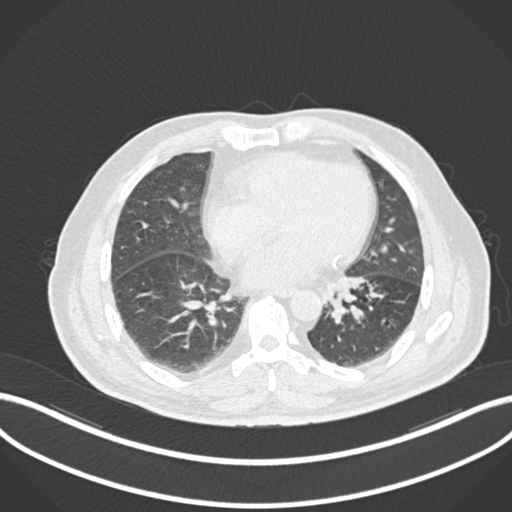
Chest CT, one axial slice. Position 41 of 161 along the scan axis. Reconstruction kernel B30f. Lung window (W 1500 / L -600 HU). 512 × 512 image matrix. Male patient, age 71 years. From the clinical record (not read from this slice): clinical TNM (as recorded): T1b N0 M0.
Structures marked on this image (rectangle marked by the reading radiologist):
- lung tumour (recorded histology: squamous cell carcinoma): bounding box (x1, y1, x2, y2) in pixels: (320, 278, 349, 325)